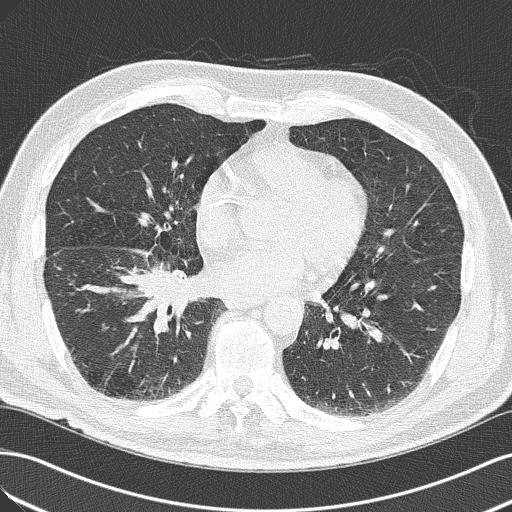
Chest CT (low-dose screening protocol), one axial image. Baseline screening round. Lung window (W 1500 / L -600 HU). 2 mm slice thickness. Lung (sharp) reconstruction kernel (B50f). Slice 92 of 143 in the series. 512 × 512 image matrix, field of view 360 × 360 mm. Male, age 65 years at enrolment.
Lesion marked by an expert reader, box from (x=103, y=247) to (x=204, y=339) px. Reader record for this screening exam (exam-level; its link to the box is not recorded): non-calcified nodule or mass ≥4 mm, right upper lobe, 18 × 13 mm, spiculated (stellate) margins, soft tissue attenuation. Official screen result: positive, change unspecified: nodule(s) >= 4 mm or enlarging nodule(s), mass(es), or other non-specific abnormalities suspicious for lung cancer. Lung cancer was diagnosed 14 days after this screen: adenocarcinoma, NOS, right lower lobe, poorly differentiated (G3), stage IIIA (AJCC 6th edition), 40 mm at pathology.